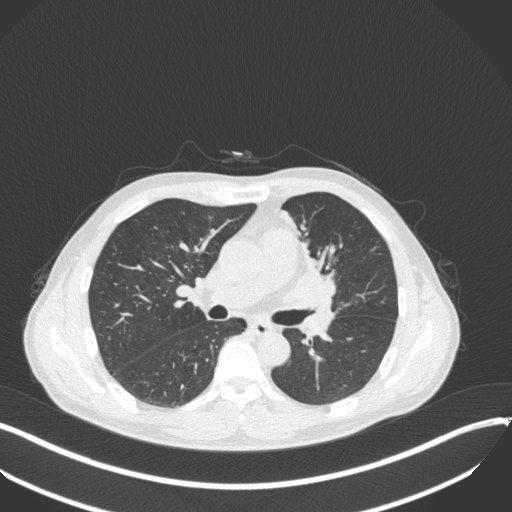
Chest CT, one axial slice; position 192 of 411 along the scan axis; reconstruction kernel B31f; 120 kVp; lung window (W 1500 / L -600 HU); 1 mm slice thickness; 512 × 512 image matrix, field of view 400 × 400 mm. Male patient, age 56 years. Case-level facts recorded for this patient, not image findings: clinical TNM (as recorded): T2a N0 M0.
Annotated regions visible in this slice (bounding box drawn by a radiologist):
- lung tumour (recorded histology: squamous cell carcinoma): bounding box <280,237,333,307> (left, top, right, bottom; pixels)